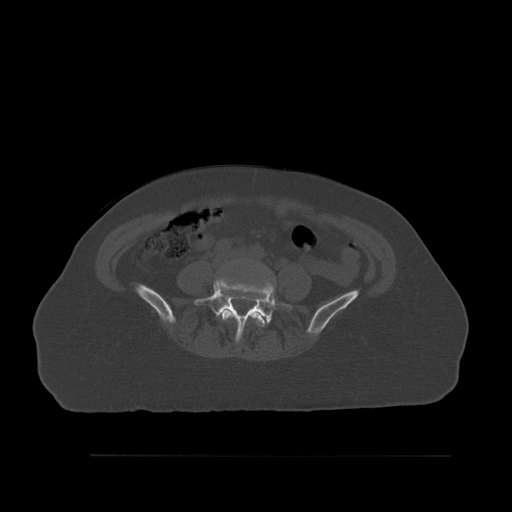
CT including the spine, one axial slice; position 194 of 527 along the scan axis; bone window (W 1800 / L 400 HU); 512 × 512 image matrix, field of view 470 × 470 mm. Female patient, age 73 years. From the clinical record (not read from this slice): primary cancer: breast; vertebrae with lytic lesions (as recorded): L2.
Structures marked on this image (semi-automatically segmented with operator editing):
- L4 vertebra: bounding box [x1, y1, x2, y2] px = [222, 305, 268, 331]
- L5 vertebra: [194, 280, 291, 342]